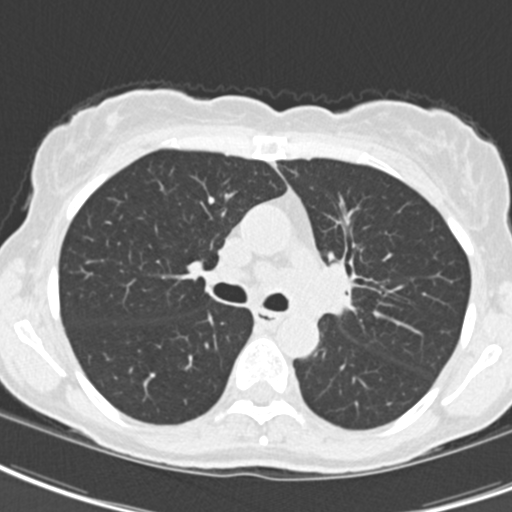
Low-dose screening chest CT, axial slice, first (baseline) screen, lung window (W 1500 / L -600 HU), standard (soft-tissue) reconstruction kernel (B30f), slice 63 of 189 in the series, 512 × 512 image matrix. Female, age 62 years at enrolment. Current smoker at enrolment.
• Expert reader's lesion annotation, bounding box [x1, y1, x2, y2] px = [295, 248, 370, 332].
• Reader record for this screening exam (exam-level; its link to the box is not recorded): non-calcified nodule or mass ≥4 mm, right upper lobe, 24 × 20 mm, smooth margins, ground glass attenuation.
• Note: the box lies in the patient's left hemithorax on this image, whereas the reader's record names the right lung; they may be different findings.
• Official screen result: positive, change unspecified: nodule(s) >= 4 mm or enlarging nodule(s), mass(es), or other non-specific abnormalities suspicious for lung cancer.